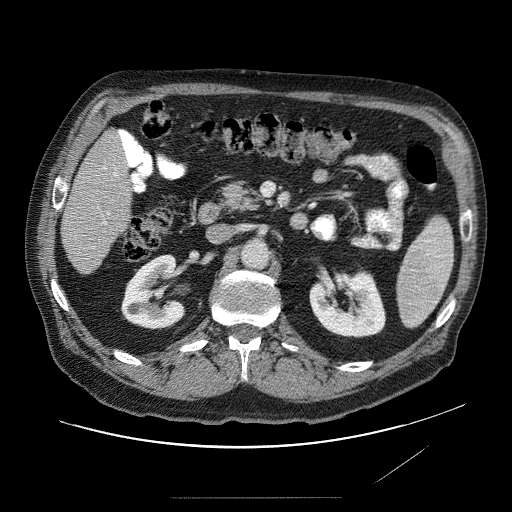
Contrast-enhanced abdominal CT (liver protocol), one axial slice. Position 21 of 89 along the scan axis. Reconstruction kernel STANDARD. 120 kVp. Soft-tissue window (W 400 / L 40 HU). 2.5 mm slice thickness. 512 × 512 image matrix, field of view 420 × 420 mm. From the clinical record (not read from this slice): diagnosis: hepatocellular carcinoma (patient treated with transarterial chemoembolisation; whether this scan precedes or follows treatment is not stated here); TNM stage (as recorded): Stage-IVA; Child-Pugh class: A; tumour differentiation: moderately differentiated; tumour nodularity: multinodular.
Annotated regions visible in this slice (semi-automatically segmented with operator editing):
- liver parenchyma outside the tumour (the mass and vessels are separate outlines, so this box may not span the whole liver): bounding box <60,122,138,278> (left, top, right, bottom; pixels)
- liver vessels: <90,125,126,242>